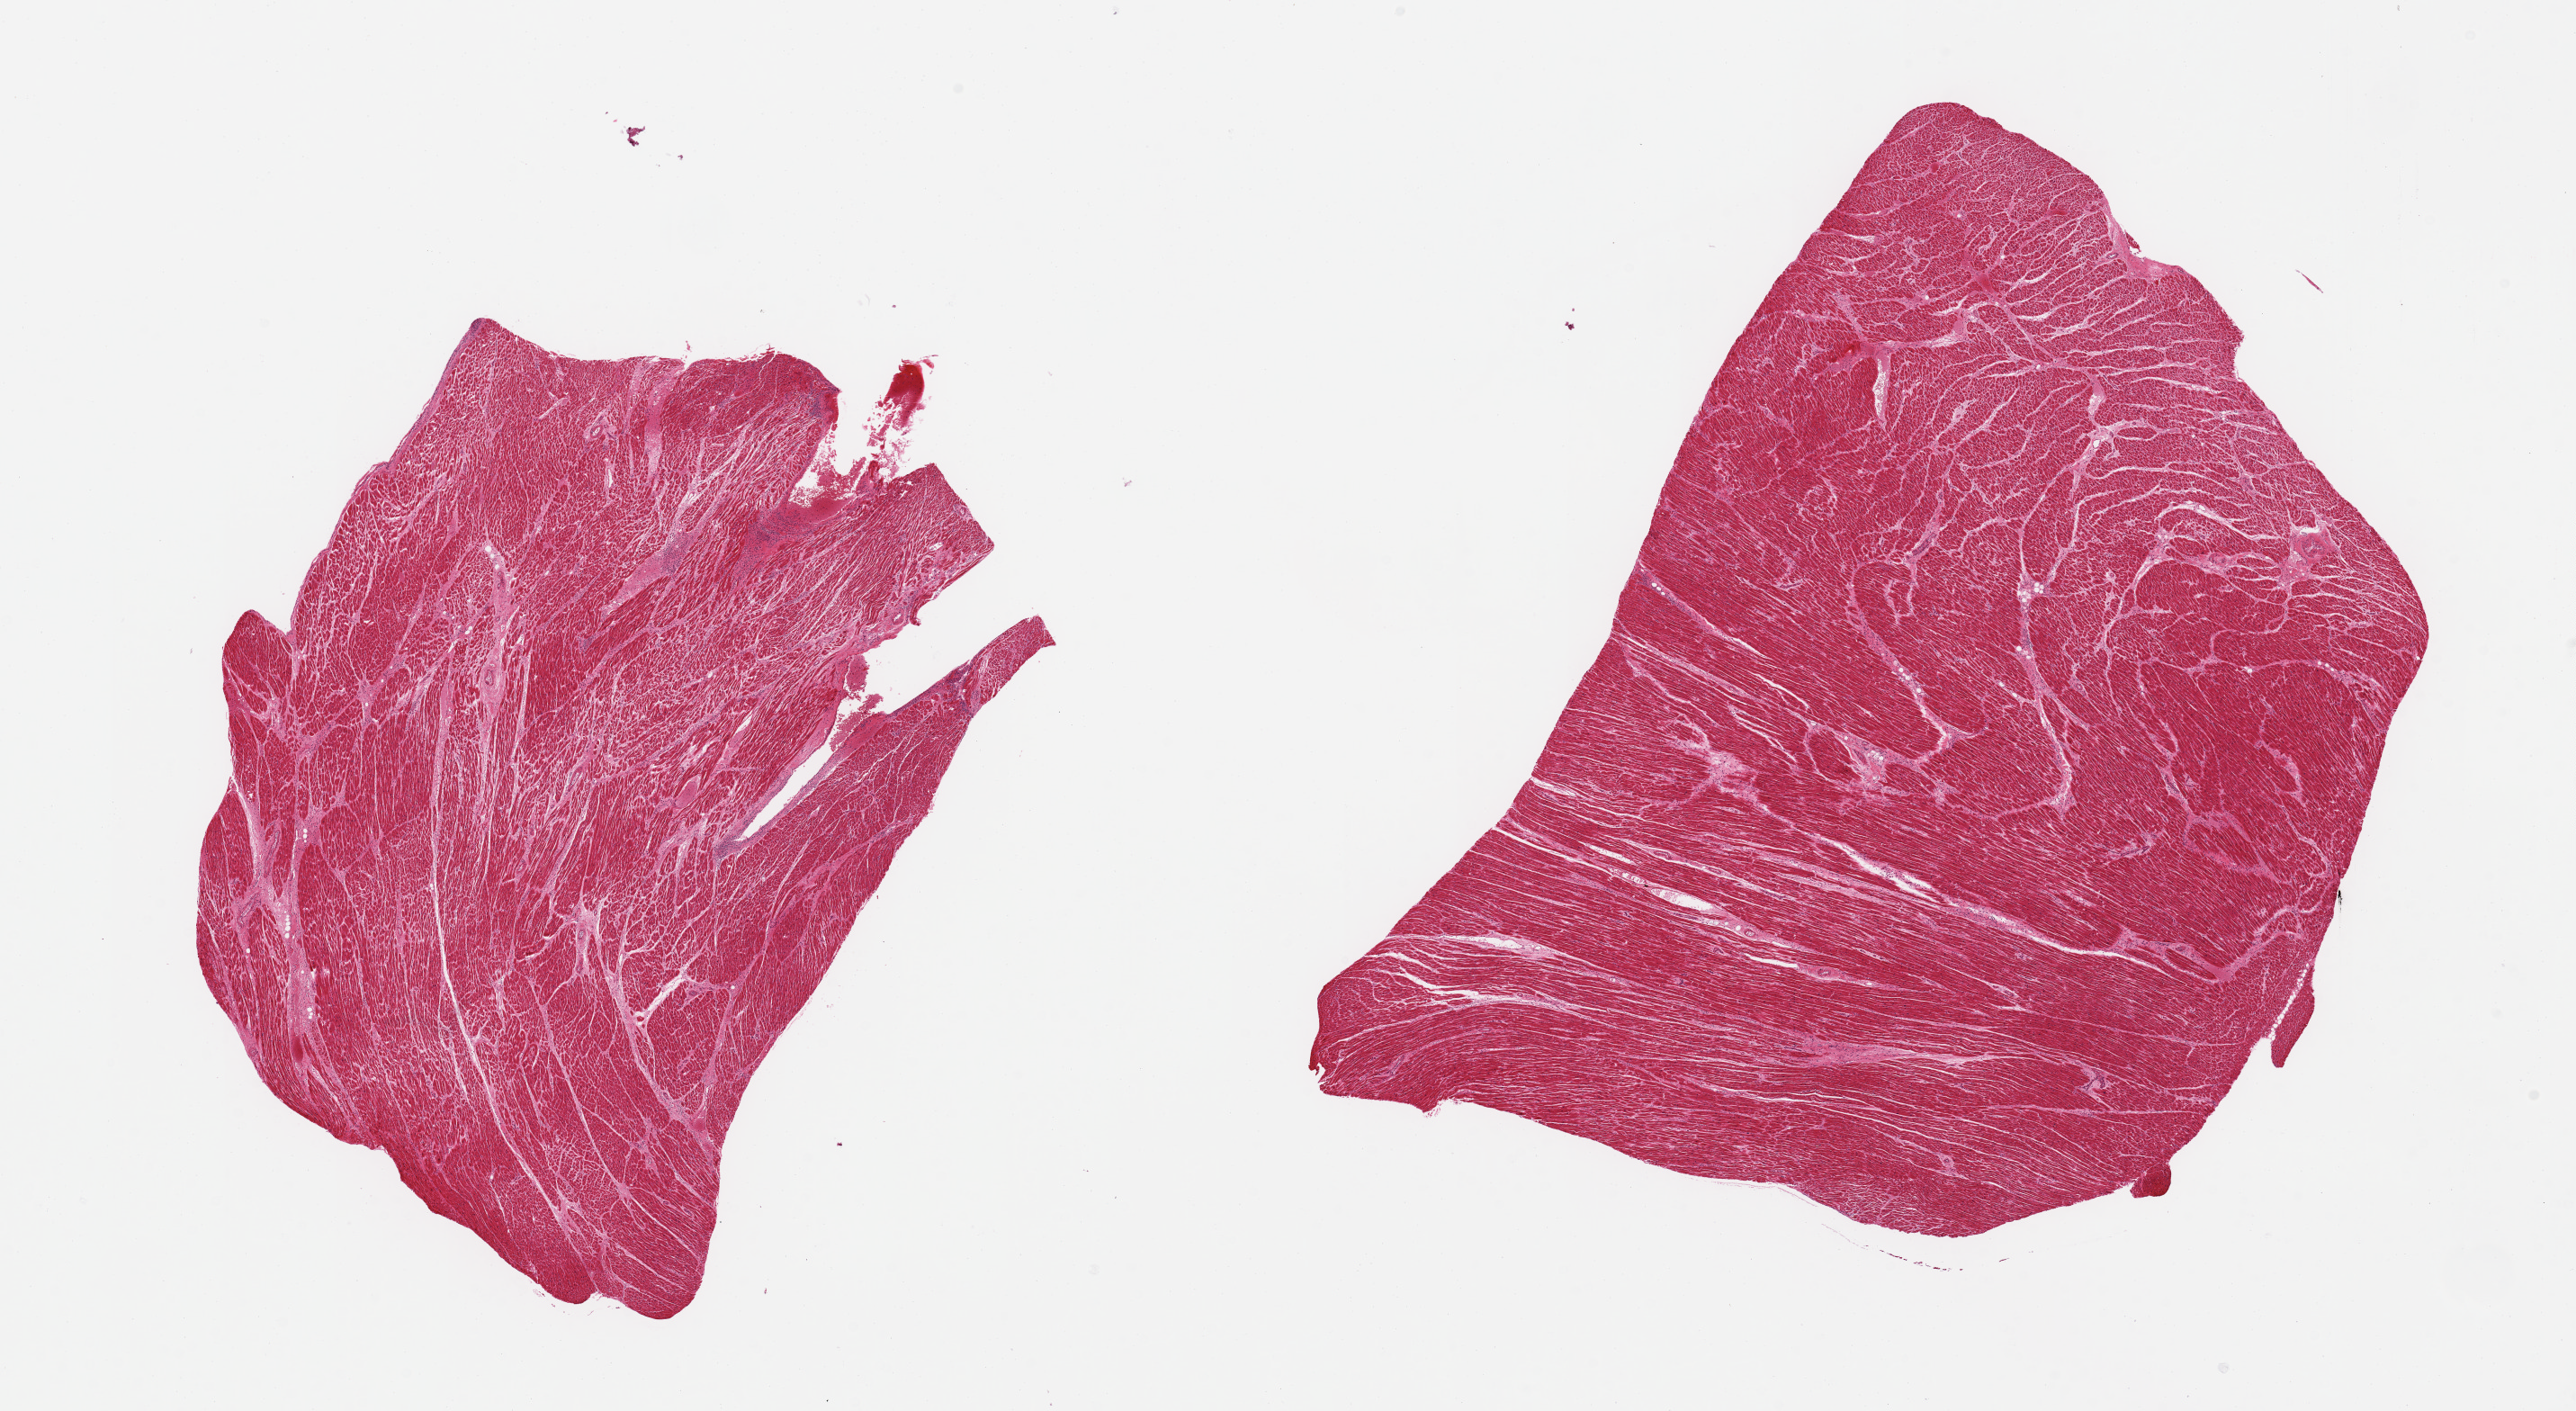
Digitized haematoxylin and eosin-stained section, brightfield, shown as a low-resolution overview of the whole scanned area (about 22.6 x 12.4 mm). PAXgene-fixed, paraffin-embedded tissue. Section of heart (target tissue). Donor tissue sample. Male donor.
Reviewer comment on this tissue sample: 2 pieces; foci of polymorphs consistent with myocardial infarction or endocarditis in 1 piece.